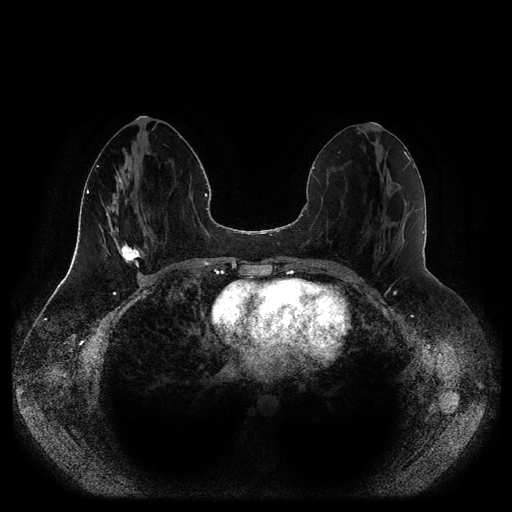
Breast MRI (dynamic contrast-enhanced, multi-phase), one axial slice. Position 43 of 116 along the scan axis. Dynamic contrast-enhanced series, time point 2 of 5 at this slice position (early post-contrast). 1.5 T. TE 2.5 ms, TR 5.2 ms. 2 mm slice thickness. 512 × 512 image matrix. Female patient, age 44 years.
Annotated regions visible in this slice (semi-automatic segmentation, software-assisted and operator-edited):
- breast lesion (labelled 'tumour' in the annotation; benign lesions carry a separate 'benign' label): bounding box (x1, y1, x2, y2) in pixels: (119, 242, 142, 268)